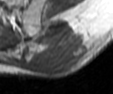
MRI of an extremity soft-tissue mass, one axial slice; position 22 of 42 along the scan axis; MR volume resampled by the dataset authors to the PET/CT grid (not the native acquisition matrix); 3.27 mm slice thickness; 113 × 94 image matrix, field of view 110 × 92 mm. Male patient. From the clinical record (not read from this slice): histological type: leiomyosarcoma; grade: intermediate; site of the primary tumour: left pelvis.
Structures marked on this image (expert contour drawn on MRI and transferred to this co-registered scan by the dataset authors):
- gross tumour volume (mass): bounding box (x1, y1, x2, y2) in pixels: (22, 18, 89, 74)